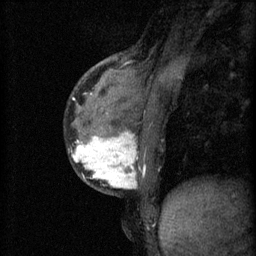
Breast MRI (dynamic contrast-enhanced), one sagittal slice; slice 25 of 60 in the series (ordered by position); 3 images stored at this slice position (order not interpretable as contrast timing); 1.5 T; TE 4.2 ms, TR 11 ms; 256 × 256 image matrix, field of view 180 × 180 mm. Female patient, age 37 years.
Structures marked on this image (semi-automatically segmented with operator editing):
- analysis volume of interest (the breast-tissue region the enhancement analysis was run in; not a lesion): bounding box [x1, y1, x2, y2] px = [70, 118, 154, 195]
- tumour enhancement mask (voxels above the 70 % enhancement threshold inside the analysis volume of interest): [72, 132, 137, 189]